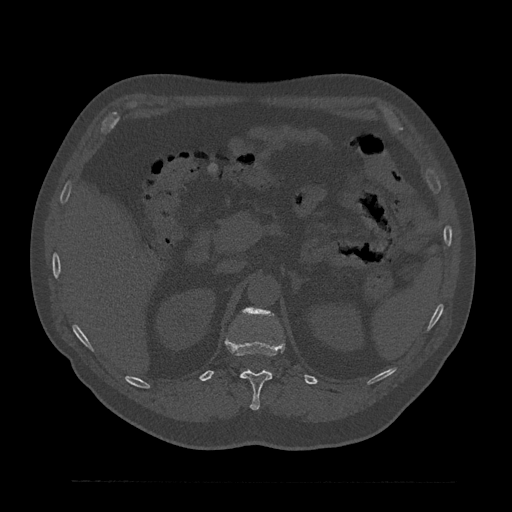
CT including the spine, one axial slice; position 212 of 797 along the scan axis; reconstruction kernel Br40s/3; 120 kVp; bone window (W 1800 / L 400 HU); 0.5 mm slice thickness; 512 × 512 image matrix, field of view 430 × 430 mm. Patient: male, 61 years. From the clinical record (not read from this slice): primary cancer: prostate.
Outlined on this slice (semi-automatically segmented with operator editing):
- L1 vertebra: bounding box <245,308,272,315> (left, top, right, bottom; pixels)
- T12 vertebra: <225,338,285,410>